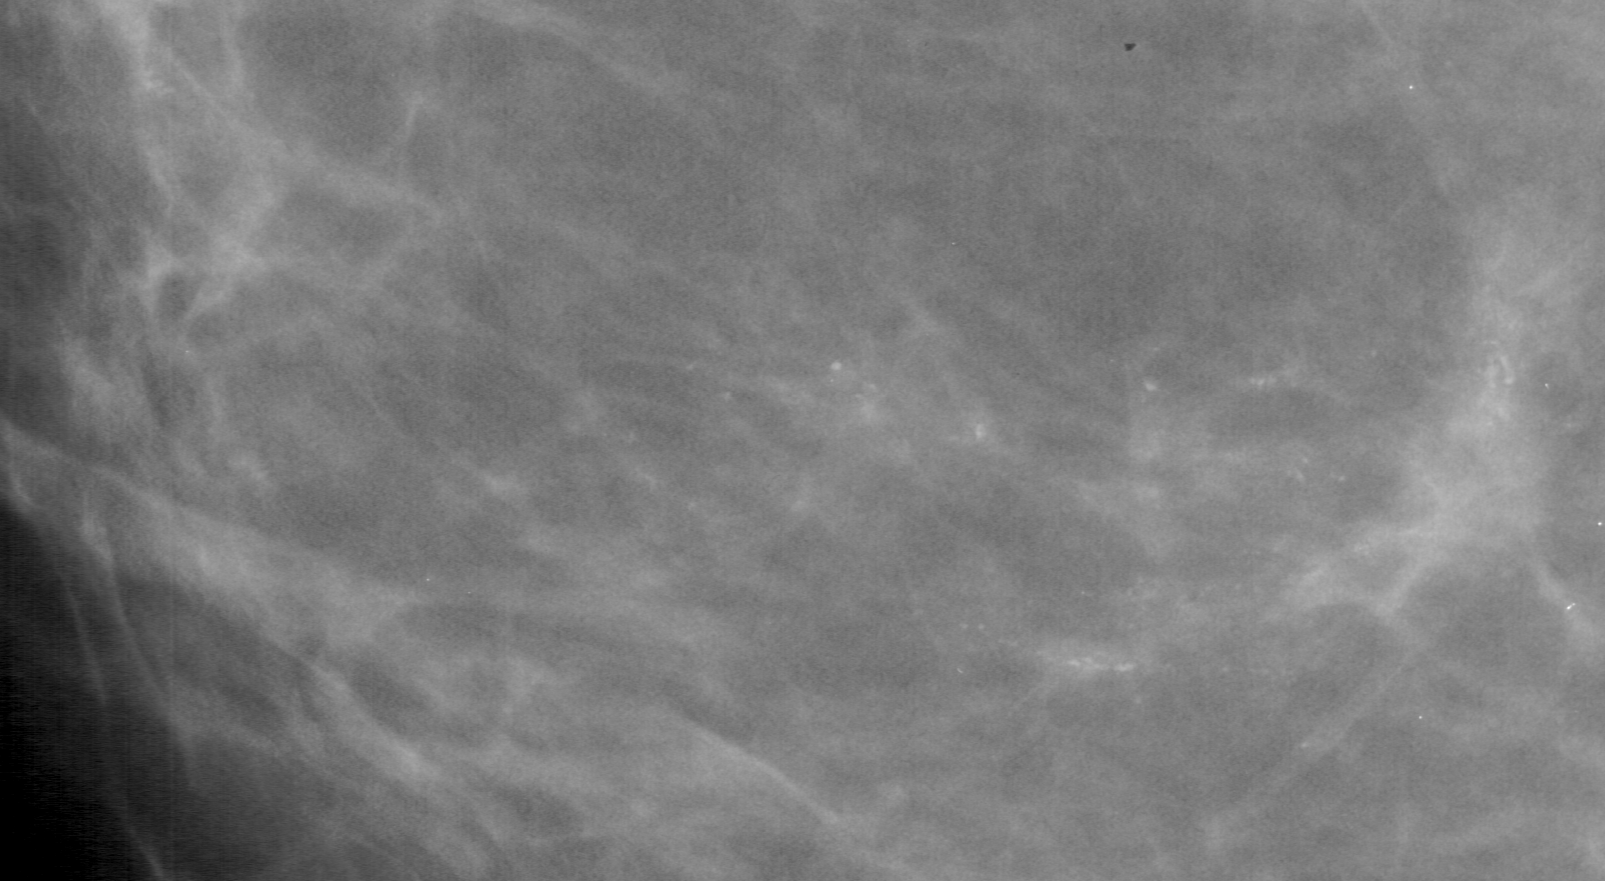
Region of interest cut from a scanned film mammogram (one marked finding), left breast, CC view, BI-RADS breast density category 3 (scale 1–4).
Calcifications, morphology pleomorphic, distribution segmental; BI-RADS assessment category 5; pathology (as recorded): malignant.